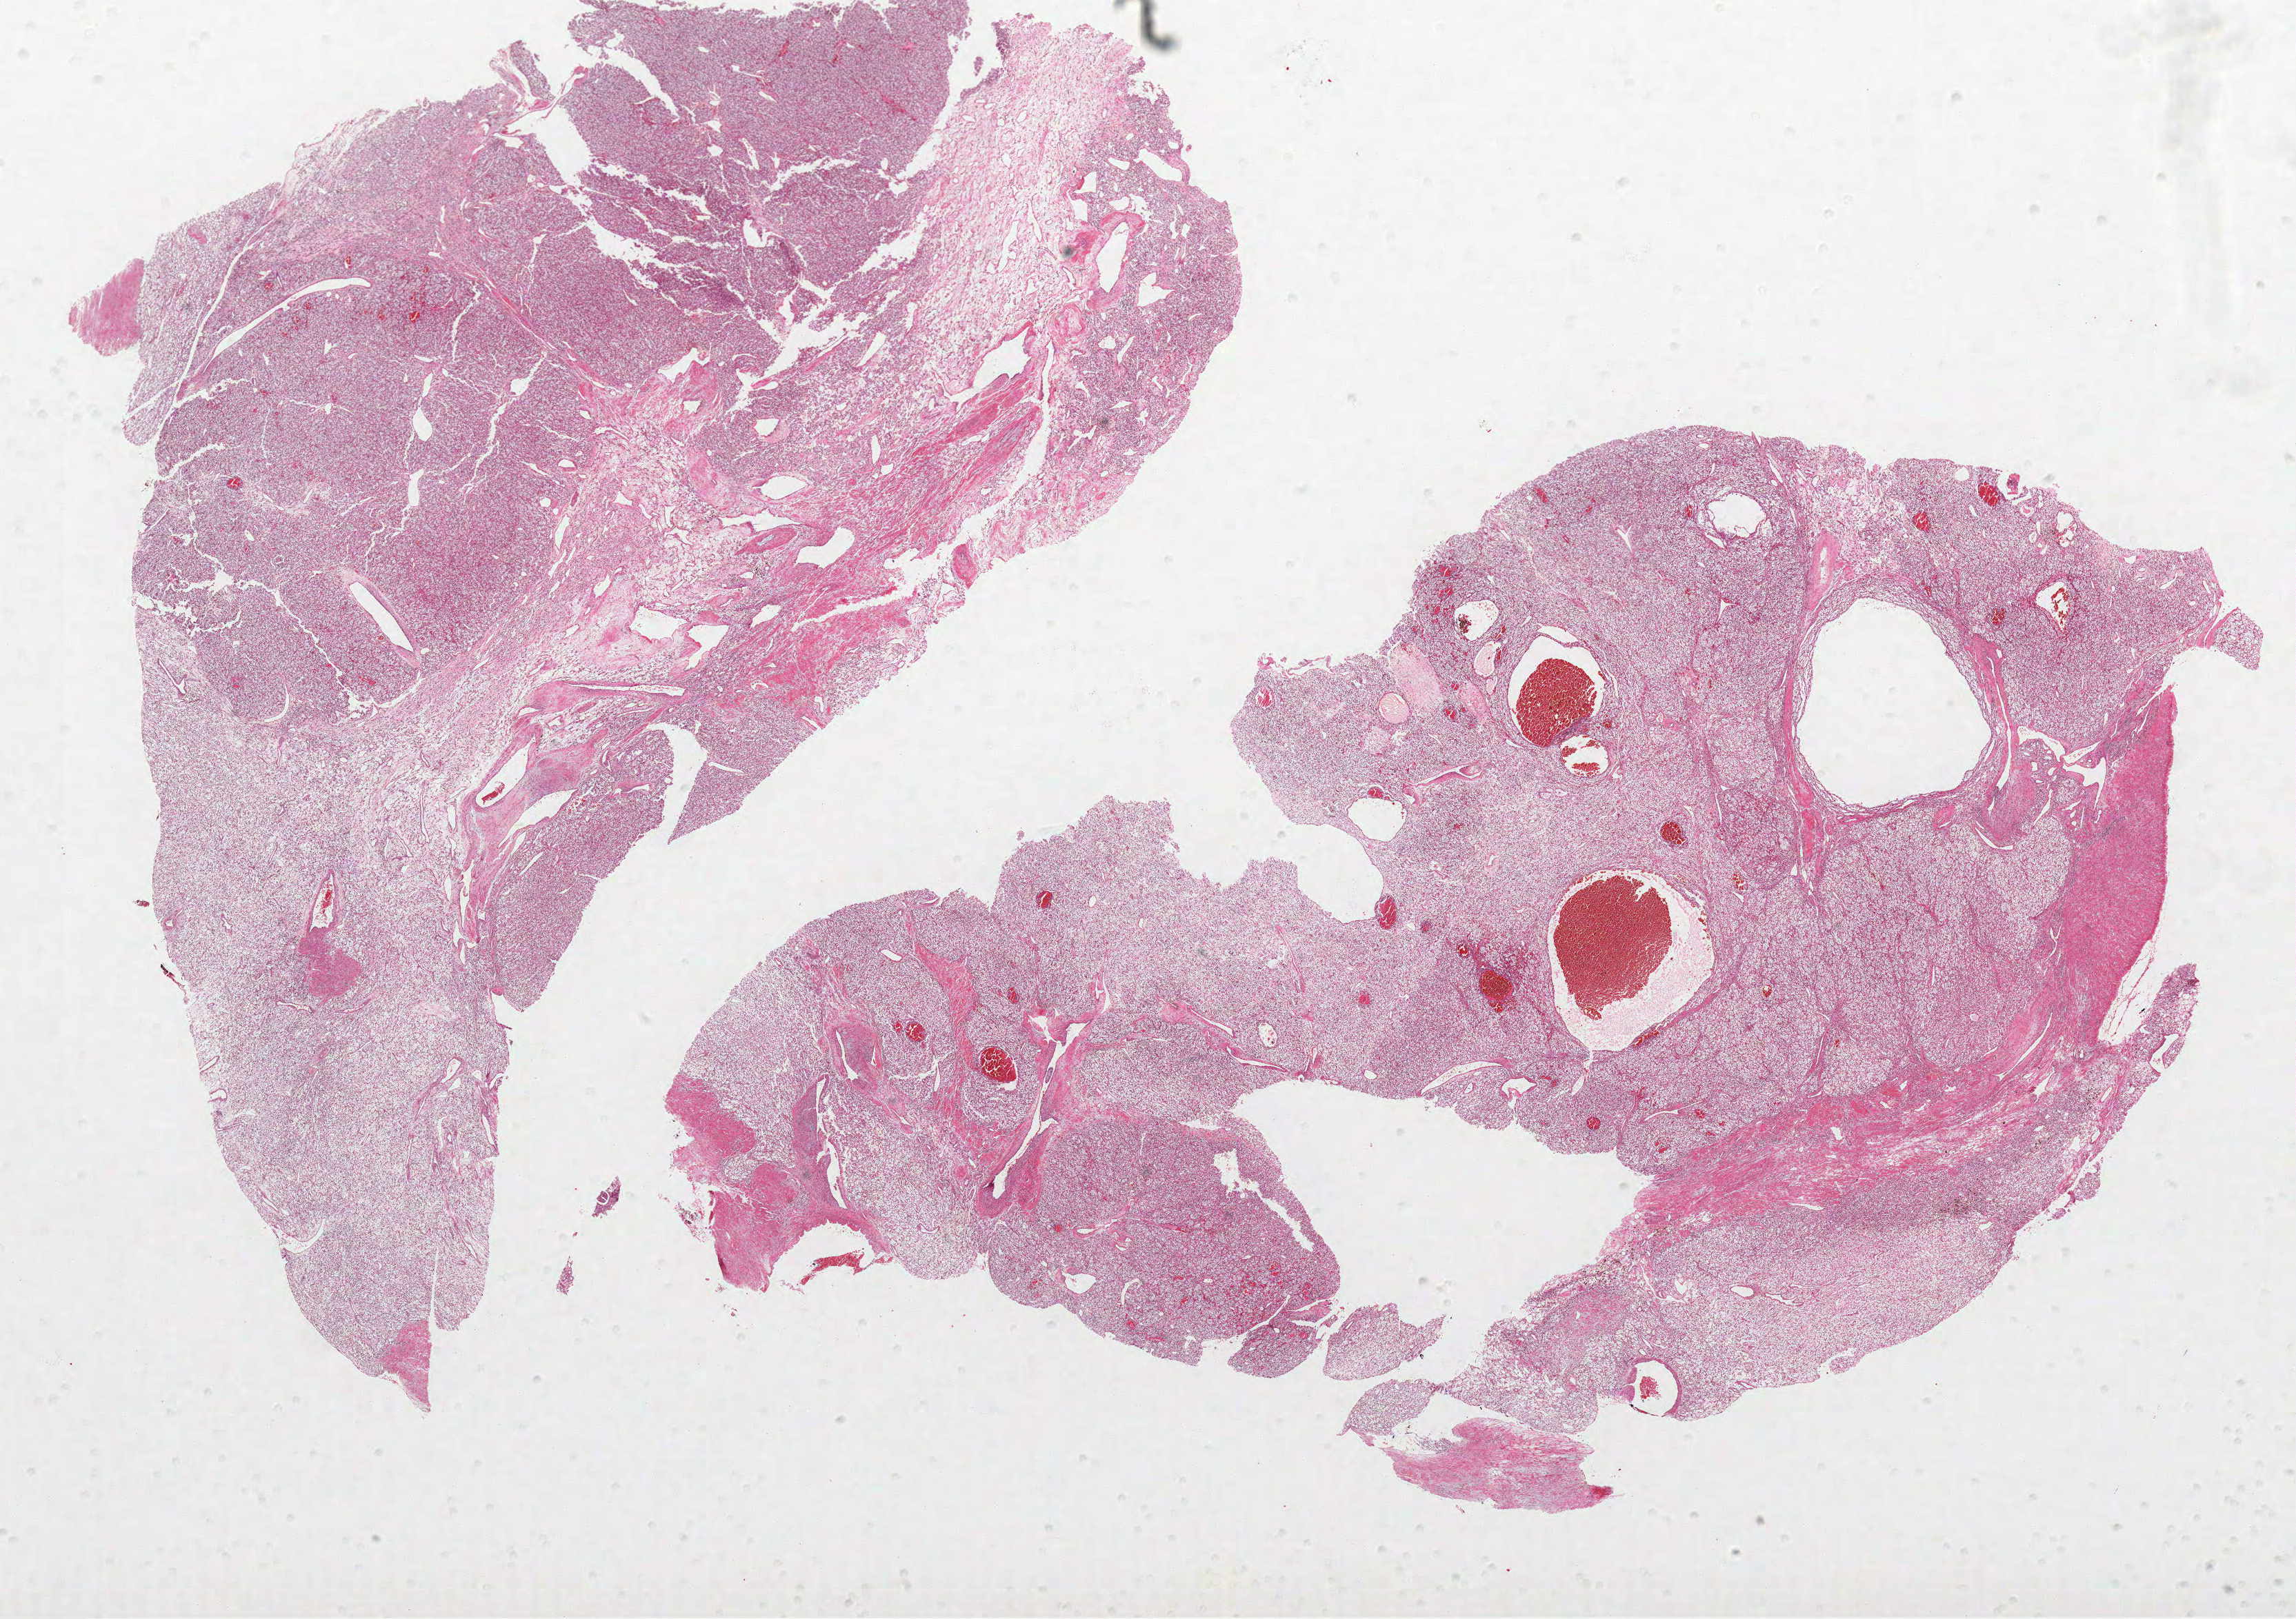
Whole-slide histology image, H&E-stained — low-resolution overview of the scanned area, about 26.6 x 18.8 mm, formalin-fixed paraffin-embedded (FFPE) diagnostic section, primary tumour sample from the kidney. Patient: male, age at initial diagnosis 47 years. Histologic grade: G2 (moderately differentiated).
• AJCC pathologic stage: I
• laterality: right
• histologic diagnosis: Clear cell adenocarcinoma, NOS